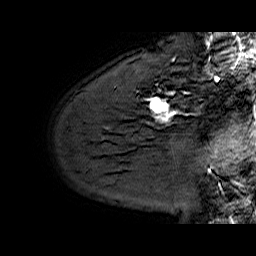
Breast MRI (dynamic contrast-enhanced), one sagittal slice. Position 48 of 60 along the scan axis. Dynamic contrast-enhanced series, time point 2 of 6 at this slice position (early post-contrast). 1.5 T. TE 6.4 ms, TR 32.9 ms. 4 mm slice thickness. 256 × 256 image matrix, field of view 200 × 200 mm. Female patient. Case-level facts recorded for this patient, not image findings: setting: breast cancer imaged before/during neoadjuvant chemotherapy; receptor status: HER2-positive.
Structures marked on this image (semi-automatic segmentation, software-assisted and operator-edited):
- analysis volume of interest (the breast-tissue region the enhancement analysis was run in; not a lesion): bounding box [x1, y1, x2, y2] px = [130, 62, 210, 128]
- tumour enhancement mask (voxels above the 100 % enhancement threshold inside the analysis volume of interest): [150, 93, 175, 122]